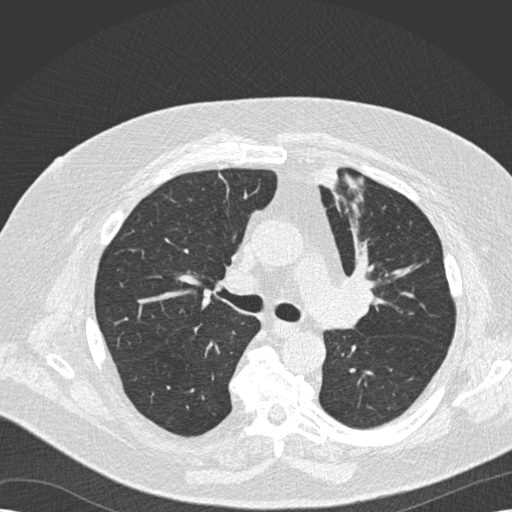
Low-dose screening chest CT, one axial slice; slice 107 of 173 in the series (ordered by position); reconstruction kernel B30f; lung window (W 1500 / L -600 HU); 2 mm slice thickness; 512 × 512 image matrix.
Structures marked on this image (manually delineated by an expert):
- lesion 1 (tumor, upper lobe of left lung): bounding box [x1, y1, x2, y2] px = [314, 160, 339, 188]